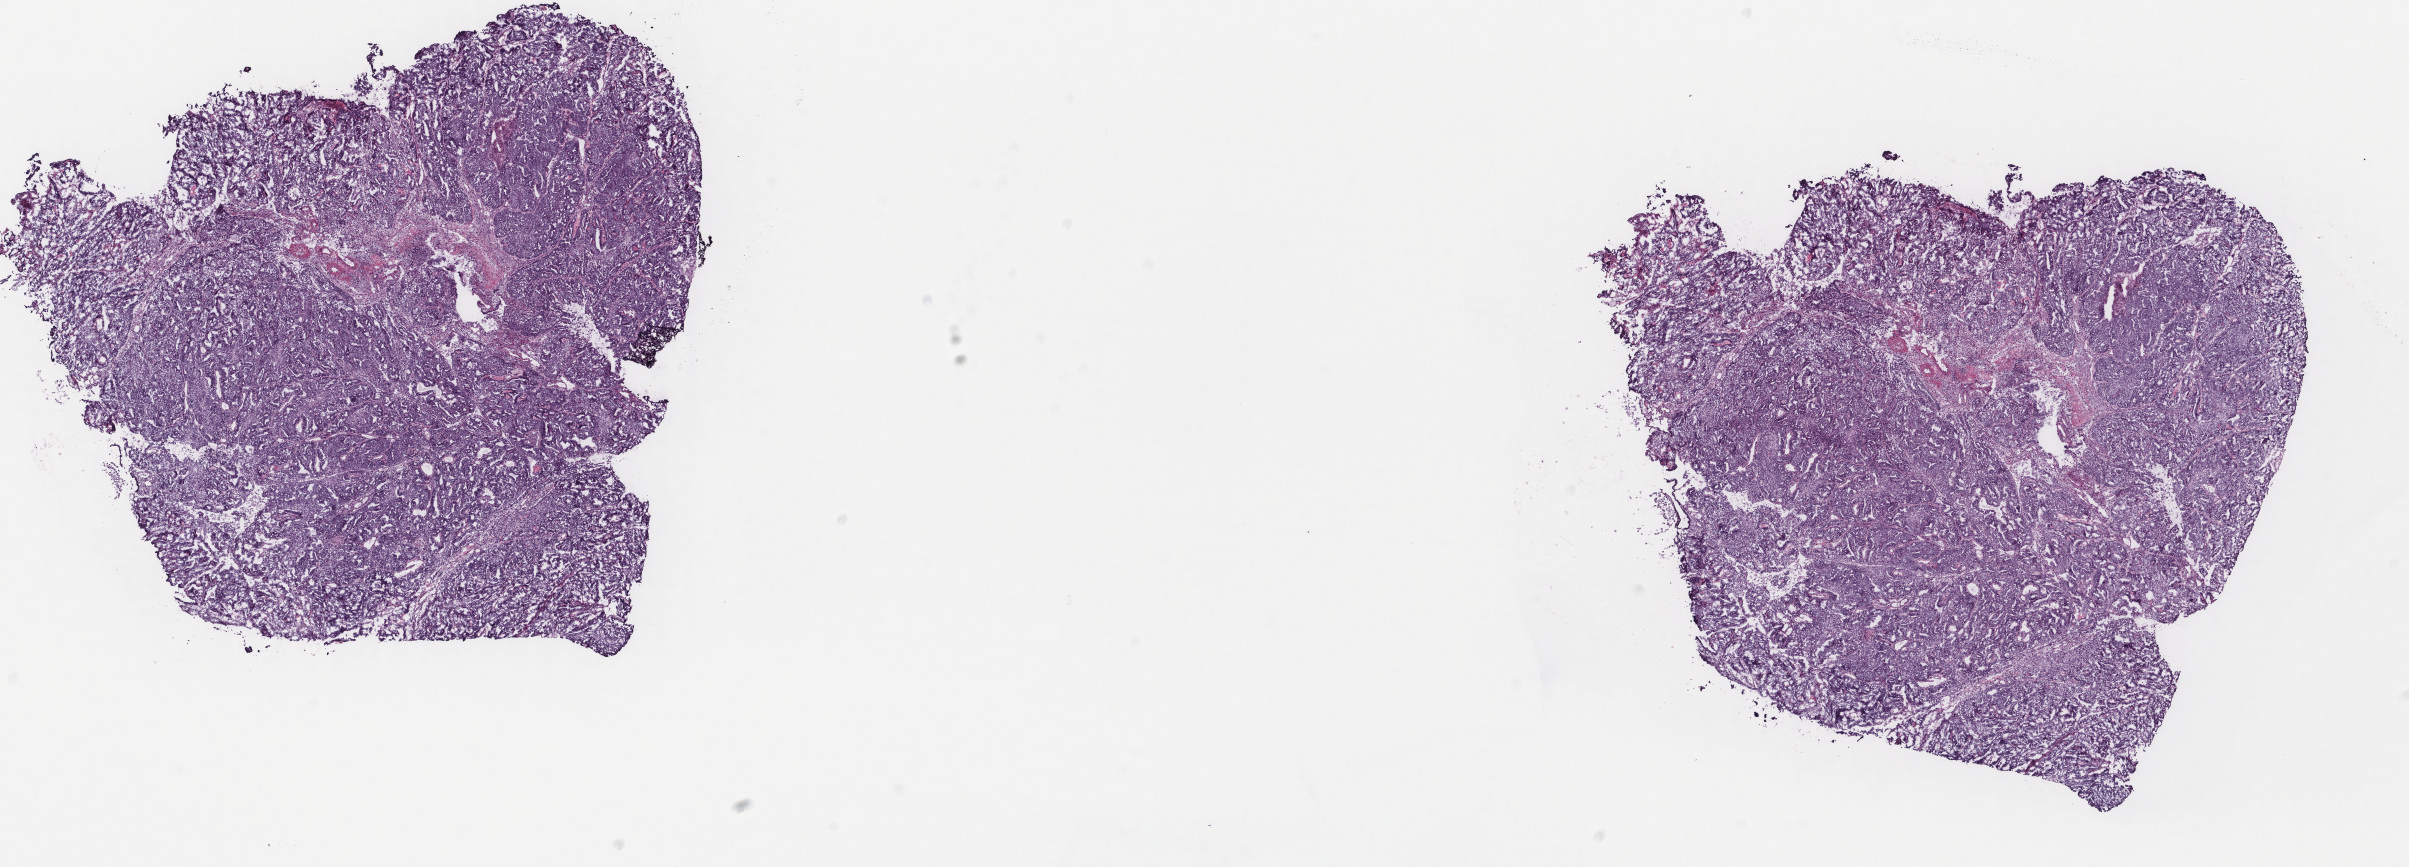
H&E-stained whole-slide image — whole scanned area (about 19.1 x 6.9 mm, from a 40x scan) shown as a low-resolution overview. Frozen section from the top of the tissue portion. Uterus, primary tumour sample. Patient: female, age at initial diagnosis 72 years. Histologic grade: G2 (moderately differentiated). Slide review estimates, as recorded: tumour cells 95%, tumour nuclei 85%, normal cells 5%, stromal cells 0%, necrosis 0%. Inflammatory infiltration, as recorded: lymphocyte infiltration 0%, monocyte infiltration 0%, neutrophil infiltration 0%.
- lymph nodes positive (case pathology): 0 of 28 examined
- diagnosis: Endometrioid adenocarcinoma, NOS
- FIGO stage: IB